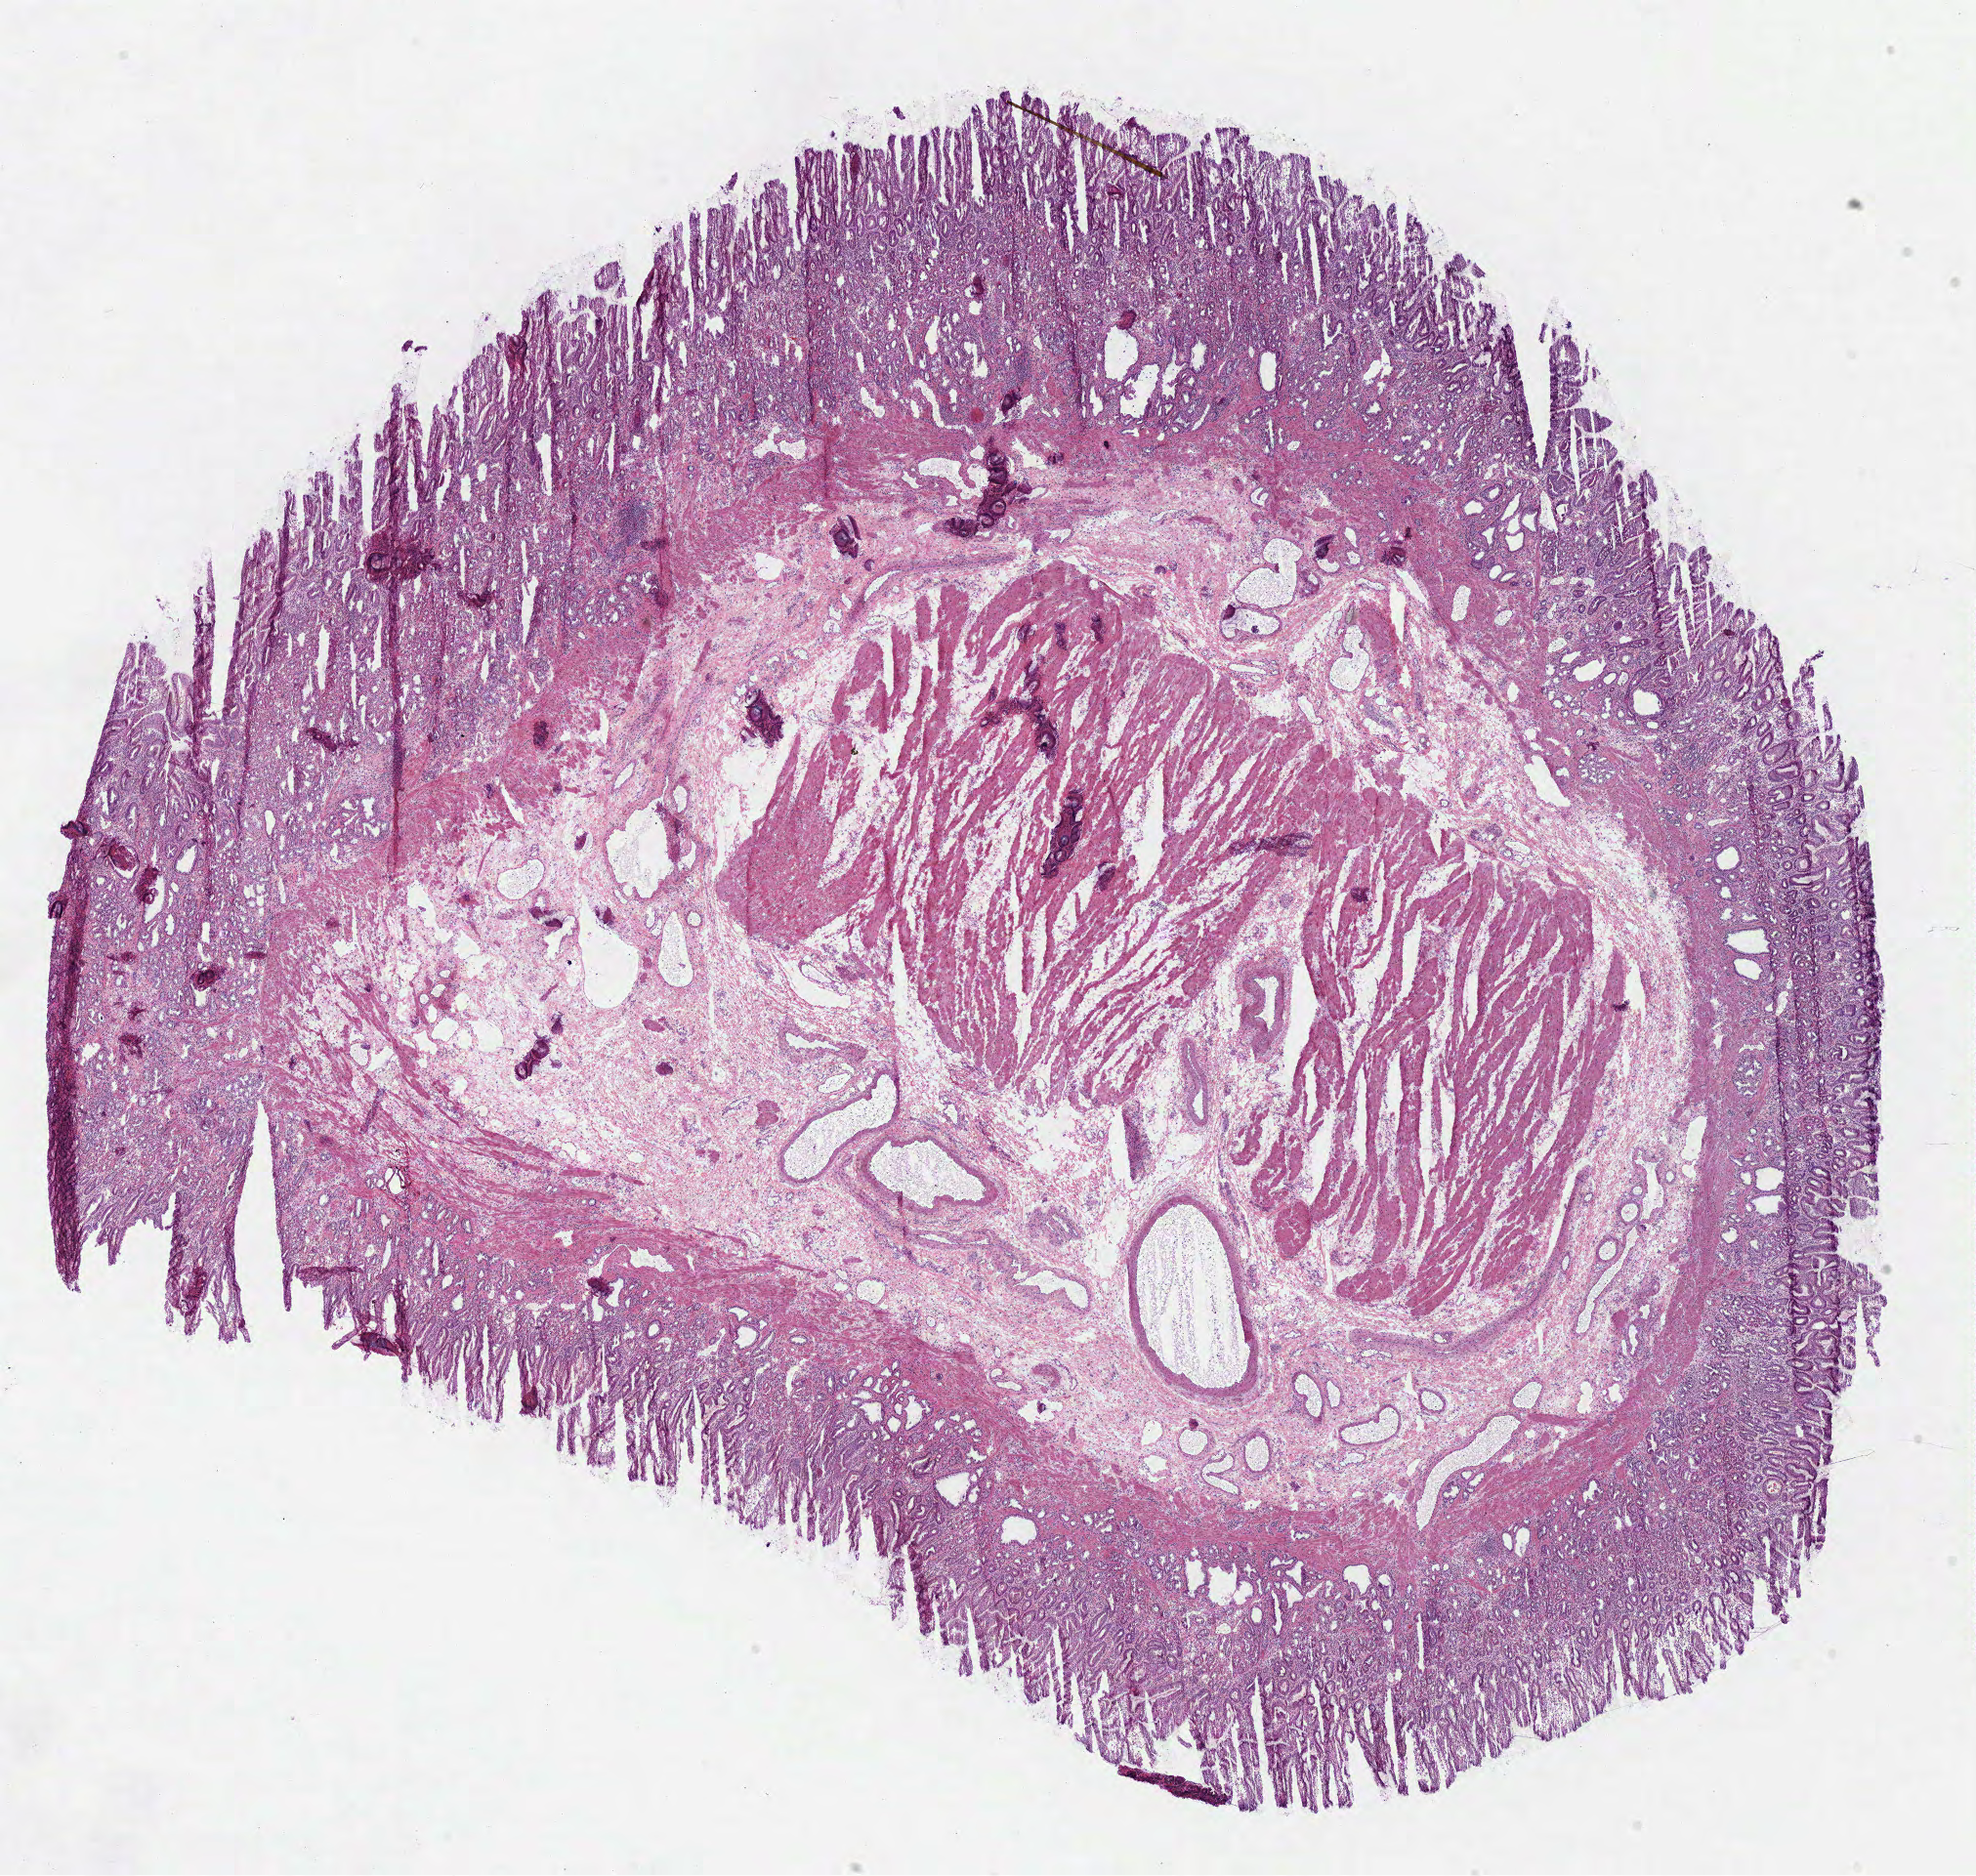
Digitized H&E-stained tissue section (whole slide), a low-resolution overview of the entire scanned area, about 15.9 x 15.1 mm (slide scanned at 40x), frozen section, solid tissue normal (non-tumour tissue) sample from the stomach. Male, age 63 years at initial diagnosis.
This section: solid tissue normal (non-tumour) sample from the same patient. Patient diagnosis: Adenocarcinoma, NOS.